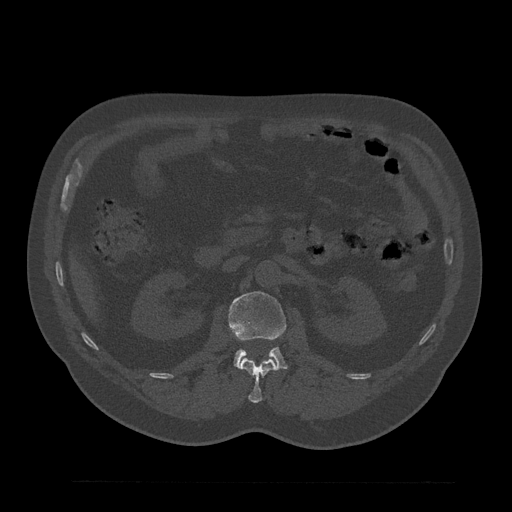
CT including the spine, one axial slice; slice 130 of 797 in the series (ordered by position); reconstruction kernel Br40s/3; 120 kVp; bone window (W 1800 / L 400 HU); 512 × 512 image matrix. Patient: male, 61 years. From the clinical record (not read from this slice): primary cancer: prostate.
Structures marked on this image (semi-automatic segmentation, software-assisted and operator-edited):
- L1 vertebra: box from (x=240, y=358) to (x=278, y=403) px
- L2 vertebra: (x=228, y=291)–(x=287, y=369)